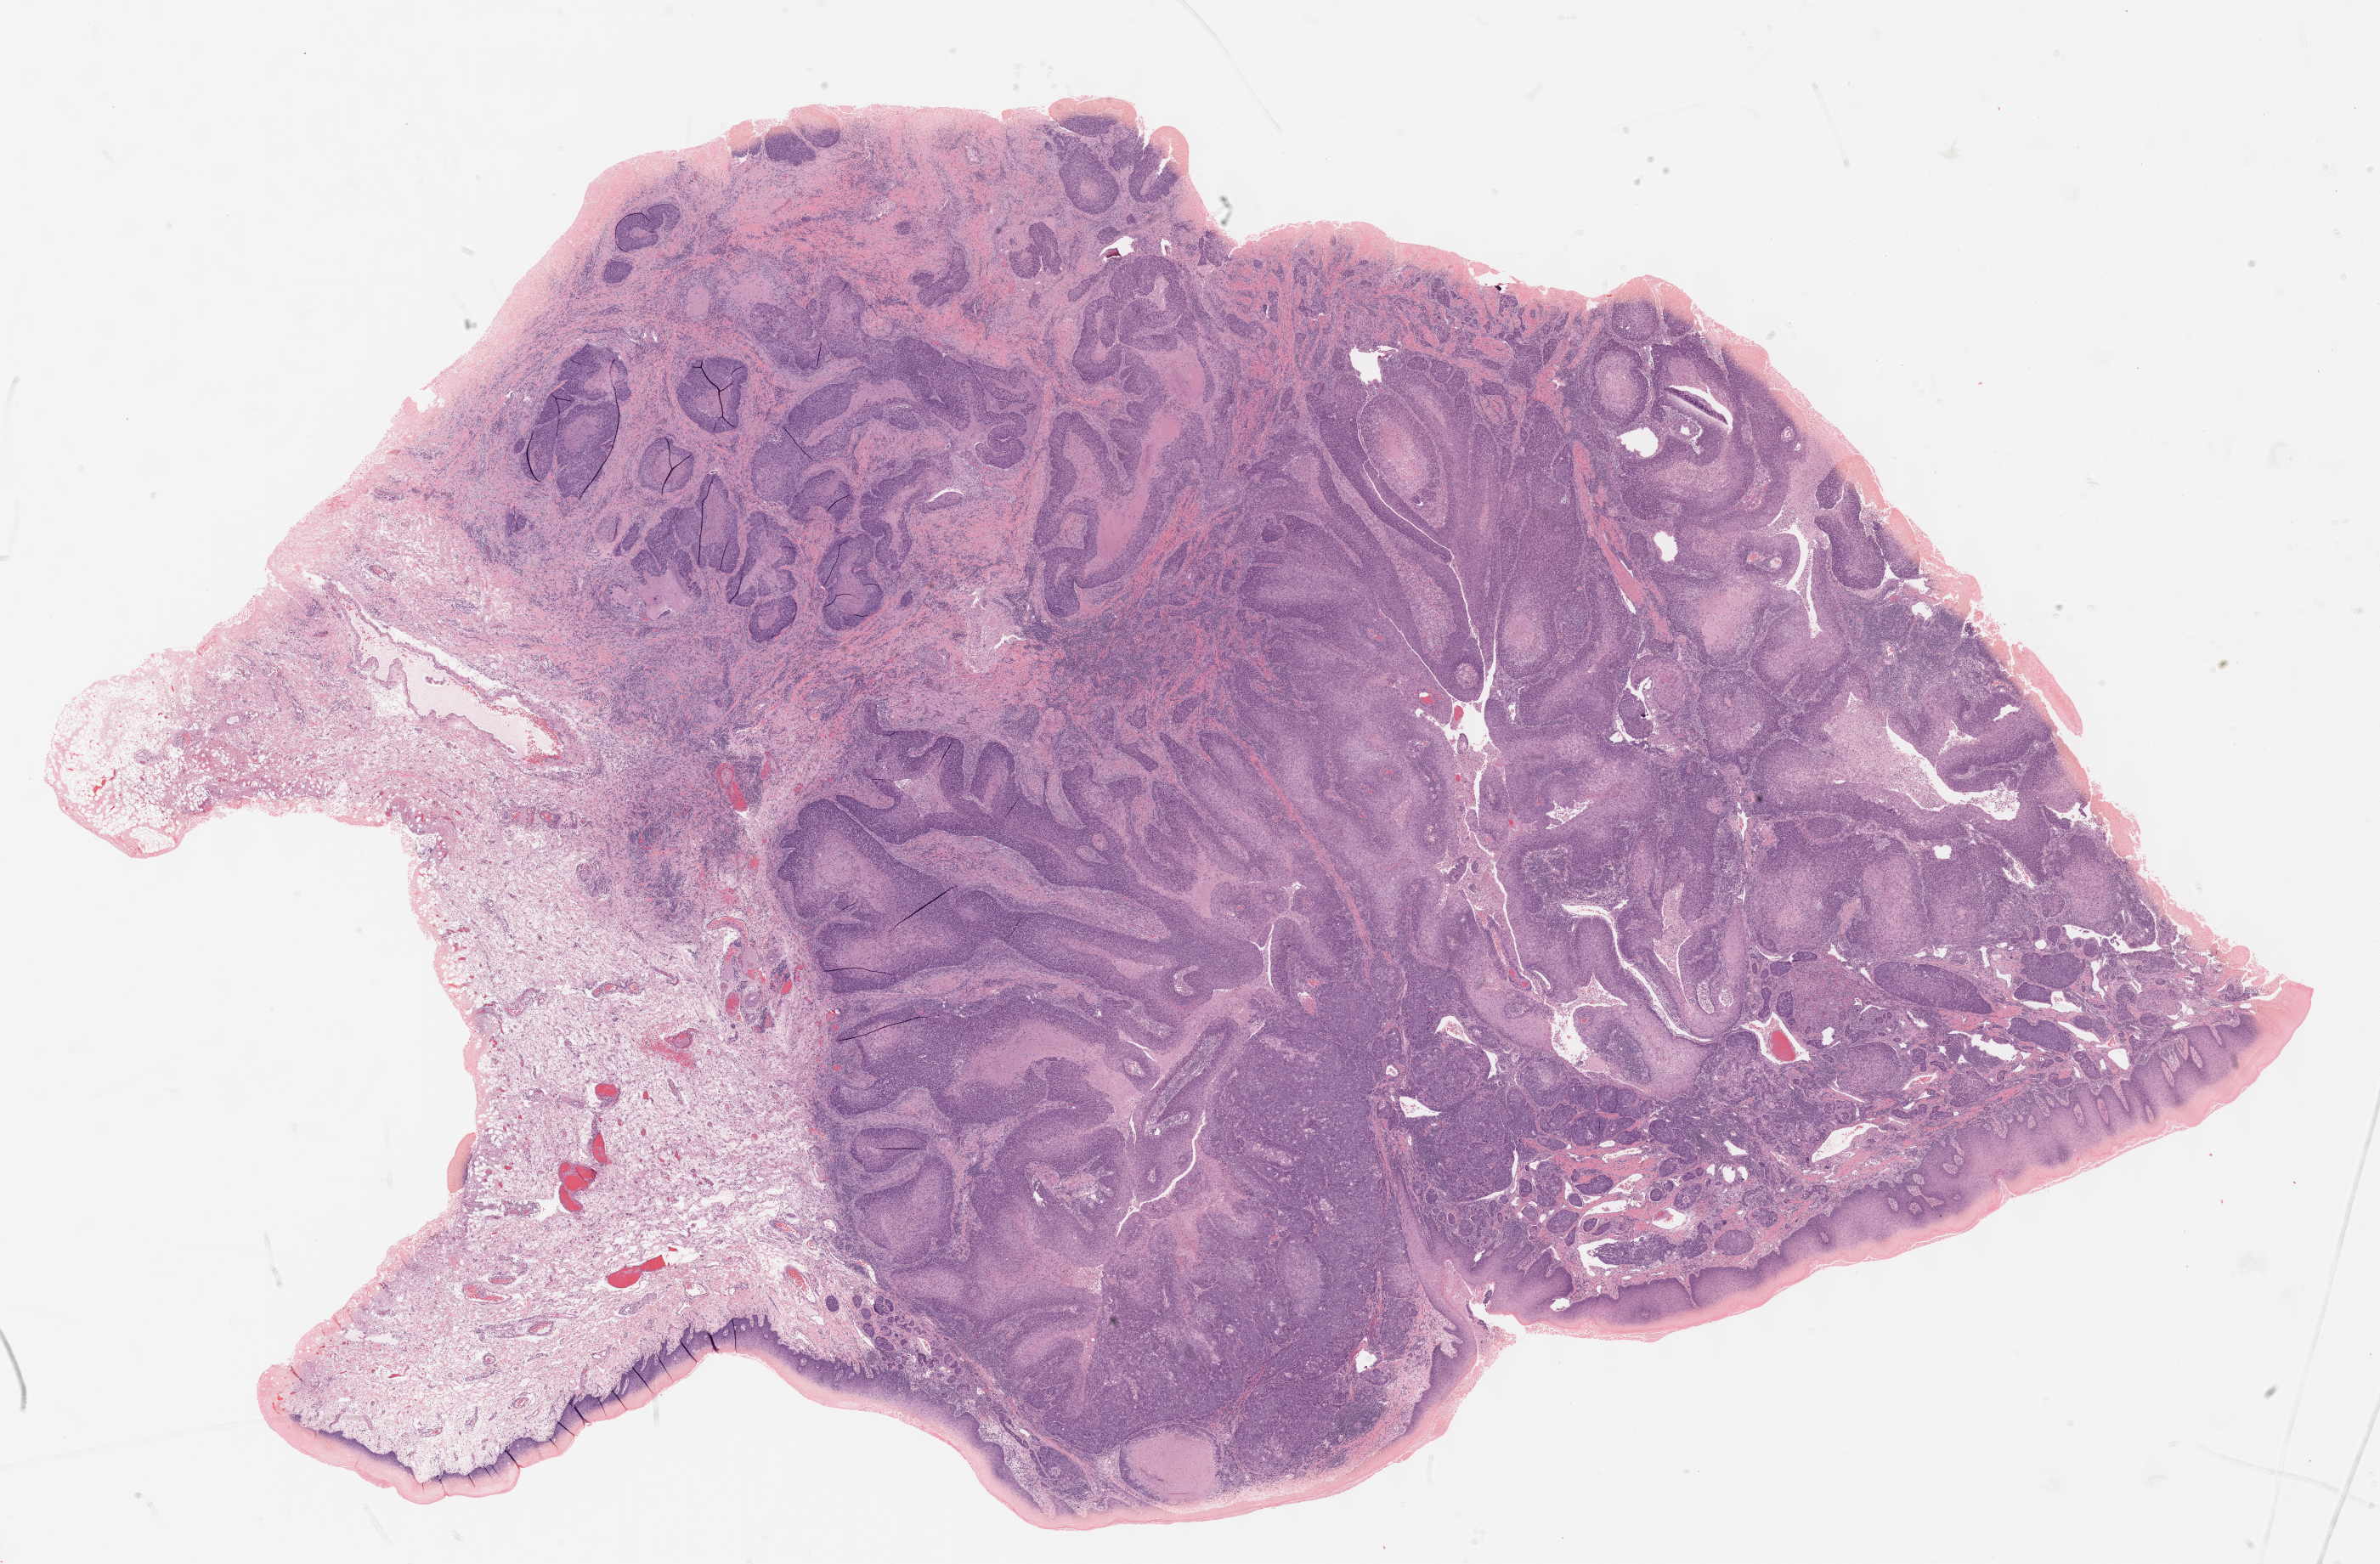
Digitized H&E-stained tissue section (whole slide) — low-resolution overview of the scanned area, about 22.6 x 14.9 mm; formalin-fixed paraffin-embedded (FFPE) diagnostic section; primary tumour sample from the head and neck. Male, age 68 years at initial diagnosis.
Pathologic diagnosis: Squamous cell carcinoma, NOS (floor of mouth, NOS).